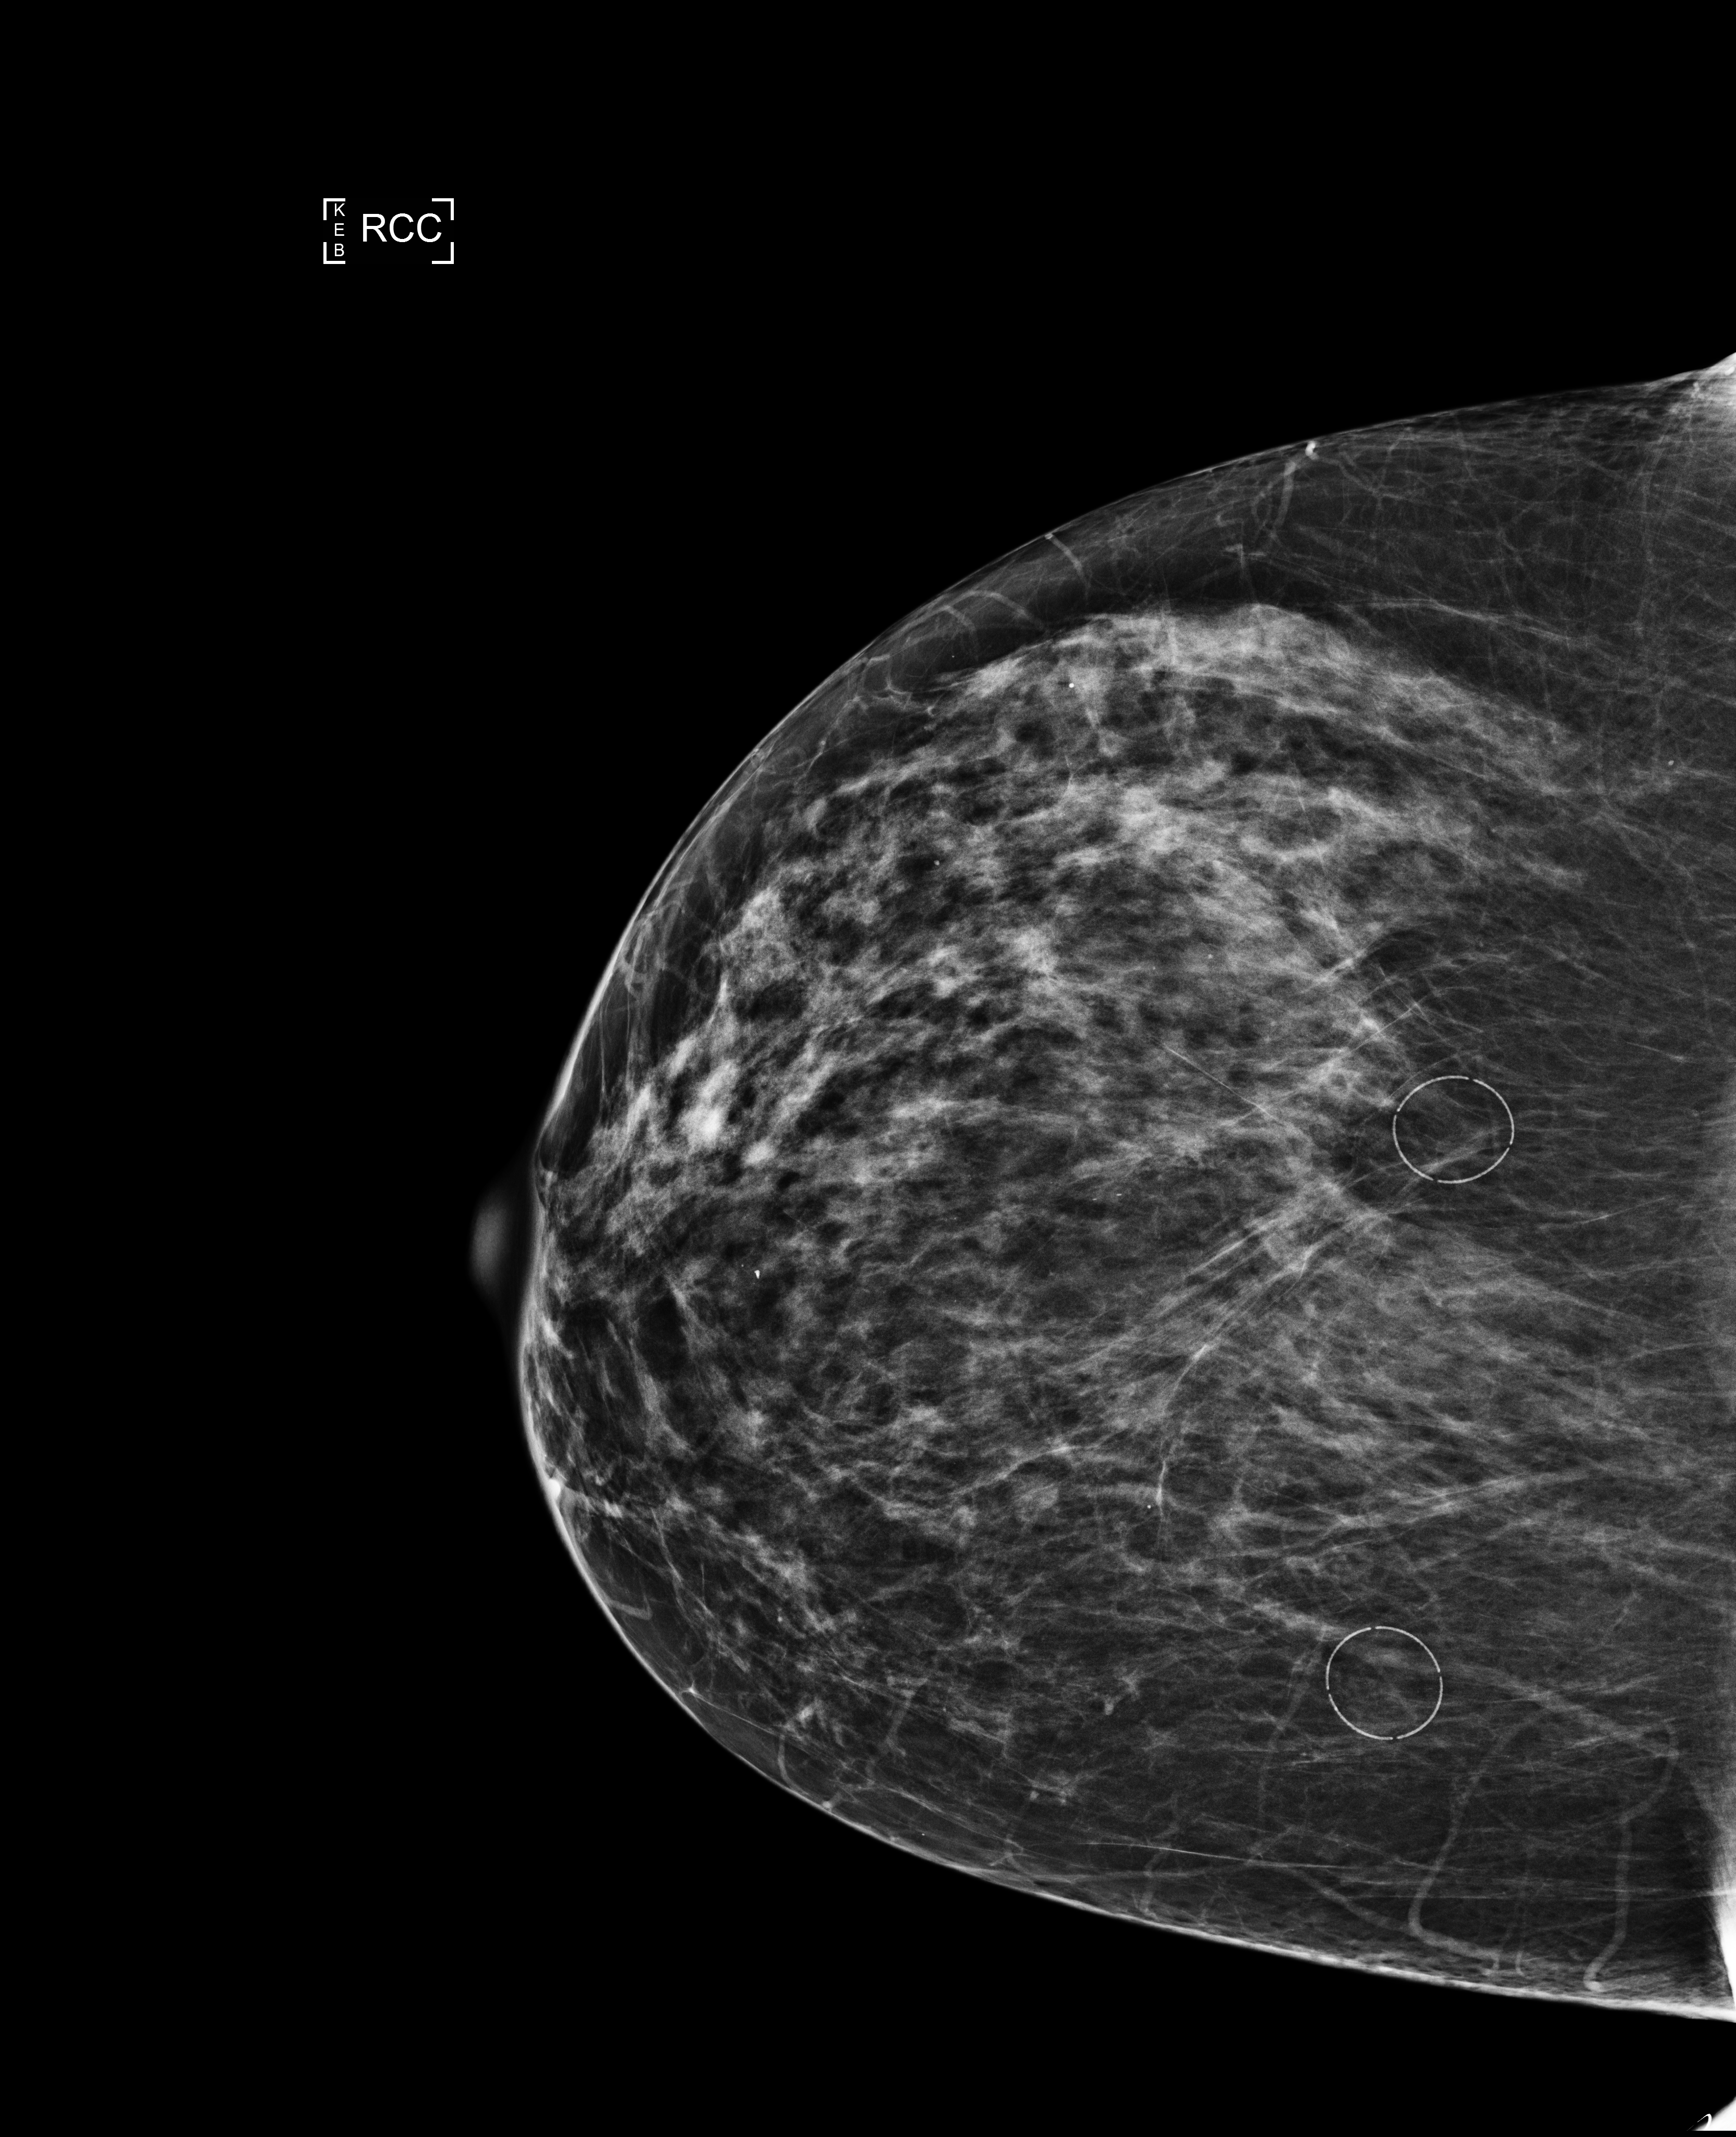
Annual screening mammography examination. Patient: female, 62 years.
Image type: full-field digital mammogram. Breast: right. Projection: craniocaudal (CC) view.